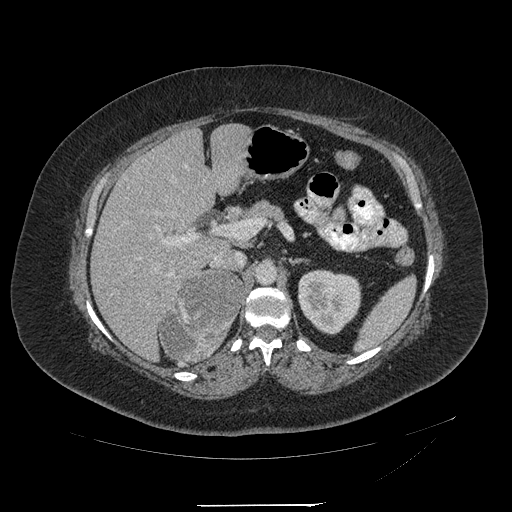
Contrast-enhanced abdominal CT, one axial slice; position 128 of 217 along the scan axis; reconstruction kernel STANDARD; intravenous contrast given; soft-tissue window (W 400 / L 40 HU); 1.25 mm slice thickness; 512 × 512 image matrix, field of view 453 × 453 mm. Female patient, age 55 years. From the clinical record (not read from this slice): diagnosis: adrenocortical carcinoma; tumour side: right adrenal; tumour size at pathology: 11 cm.
Structures marked on this image (semi-automatic segmentation, software-assisted and operator-edited):
- mass: bounding box (x1, y1, x2, y2) in pixels: (161, 271, 242, 361)